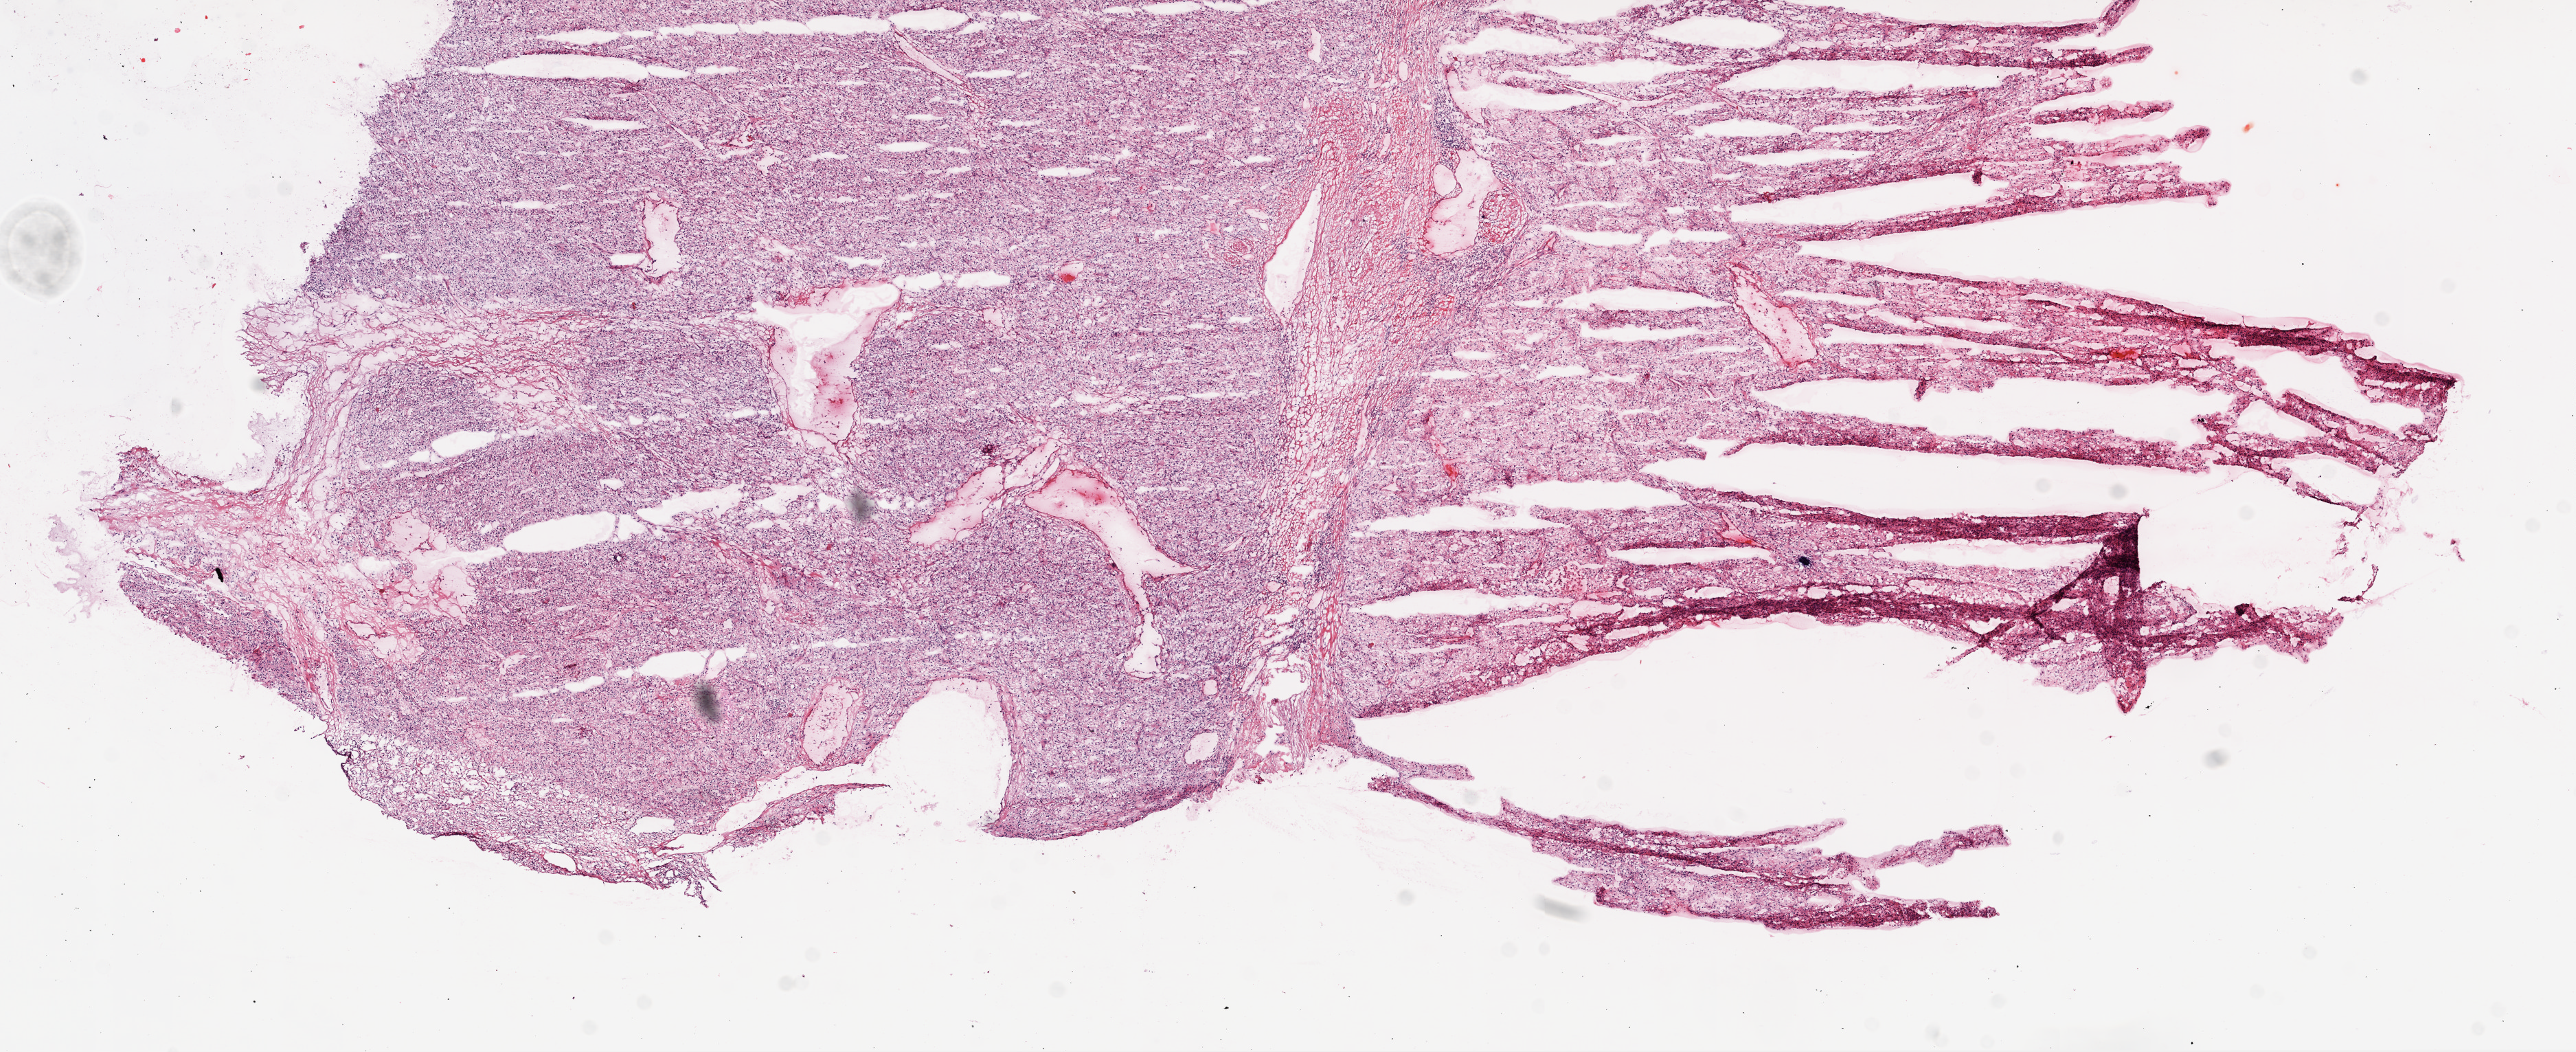
H&E-stained whole-slide image — a low-resolution overview of the entire scanned area, about 15.0 x 6.1 mm (slide scanned at 20x); frozen section from the top of the tissue portion; sample: primary tumour, kidney. Male, age 54 years at initial diagnosis. Histologic grade: G3 (poorly differentiated). Pathologist review of this section (percent, as recorded): tumour cells 90%, tumour nuclei 90%, normal cells 0%, stromal cells 10%, necrosis 0%.
- AJCC pathologic stage: III
- diagnosis: Clear cell adenocarcinoma, NOS
- TNM: T3b NX M0